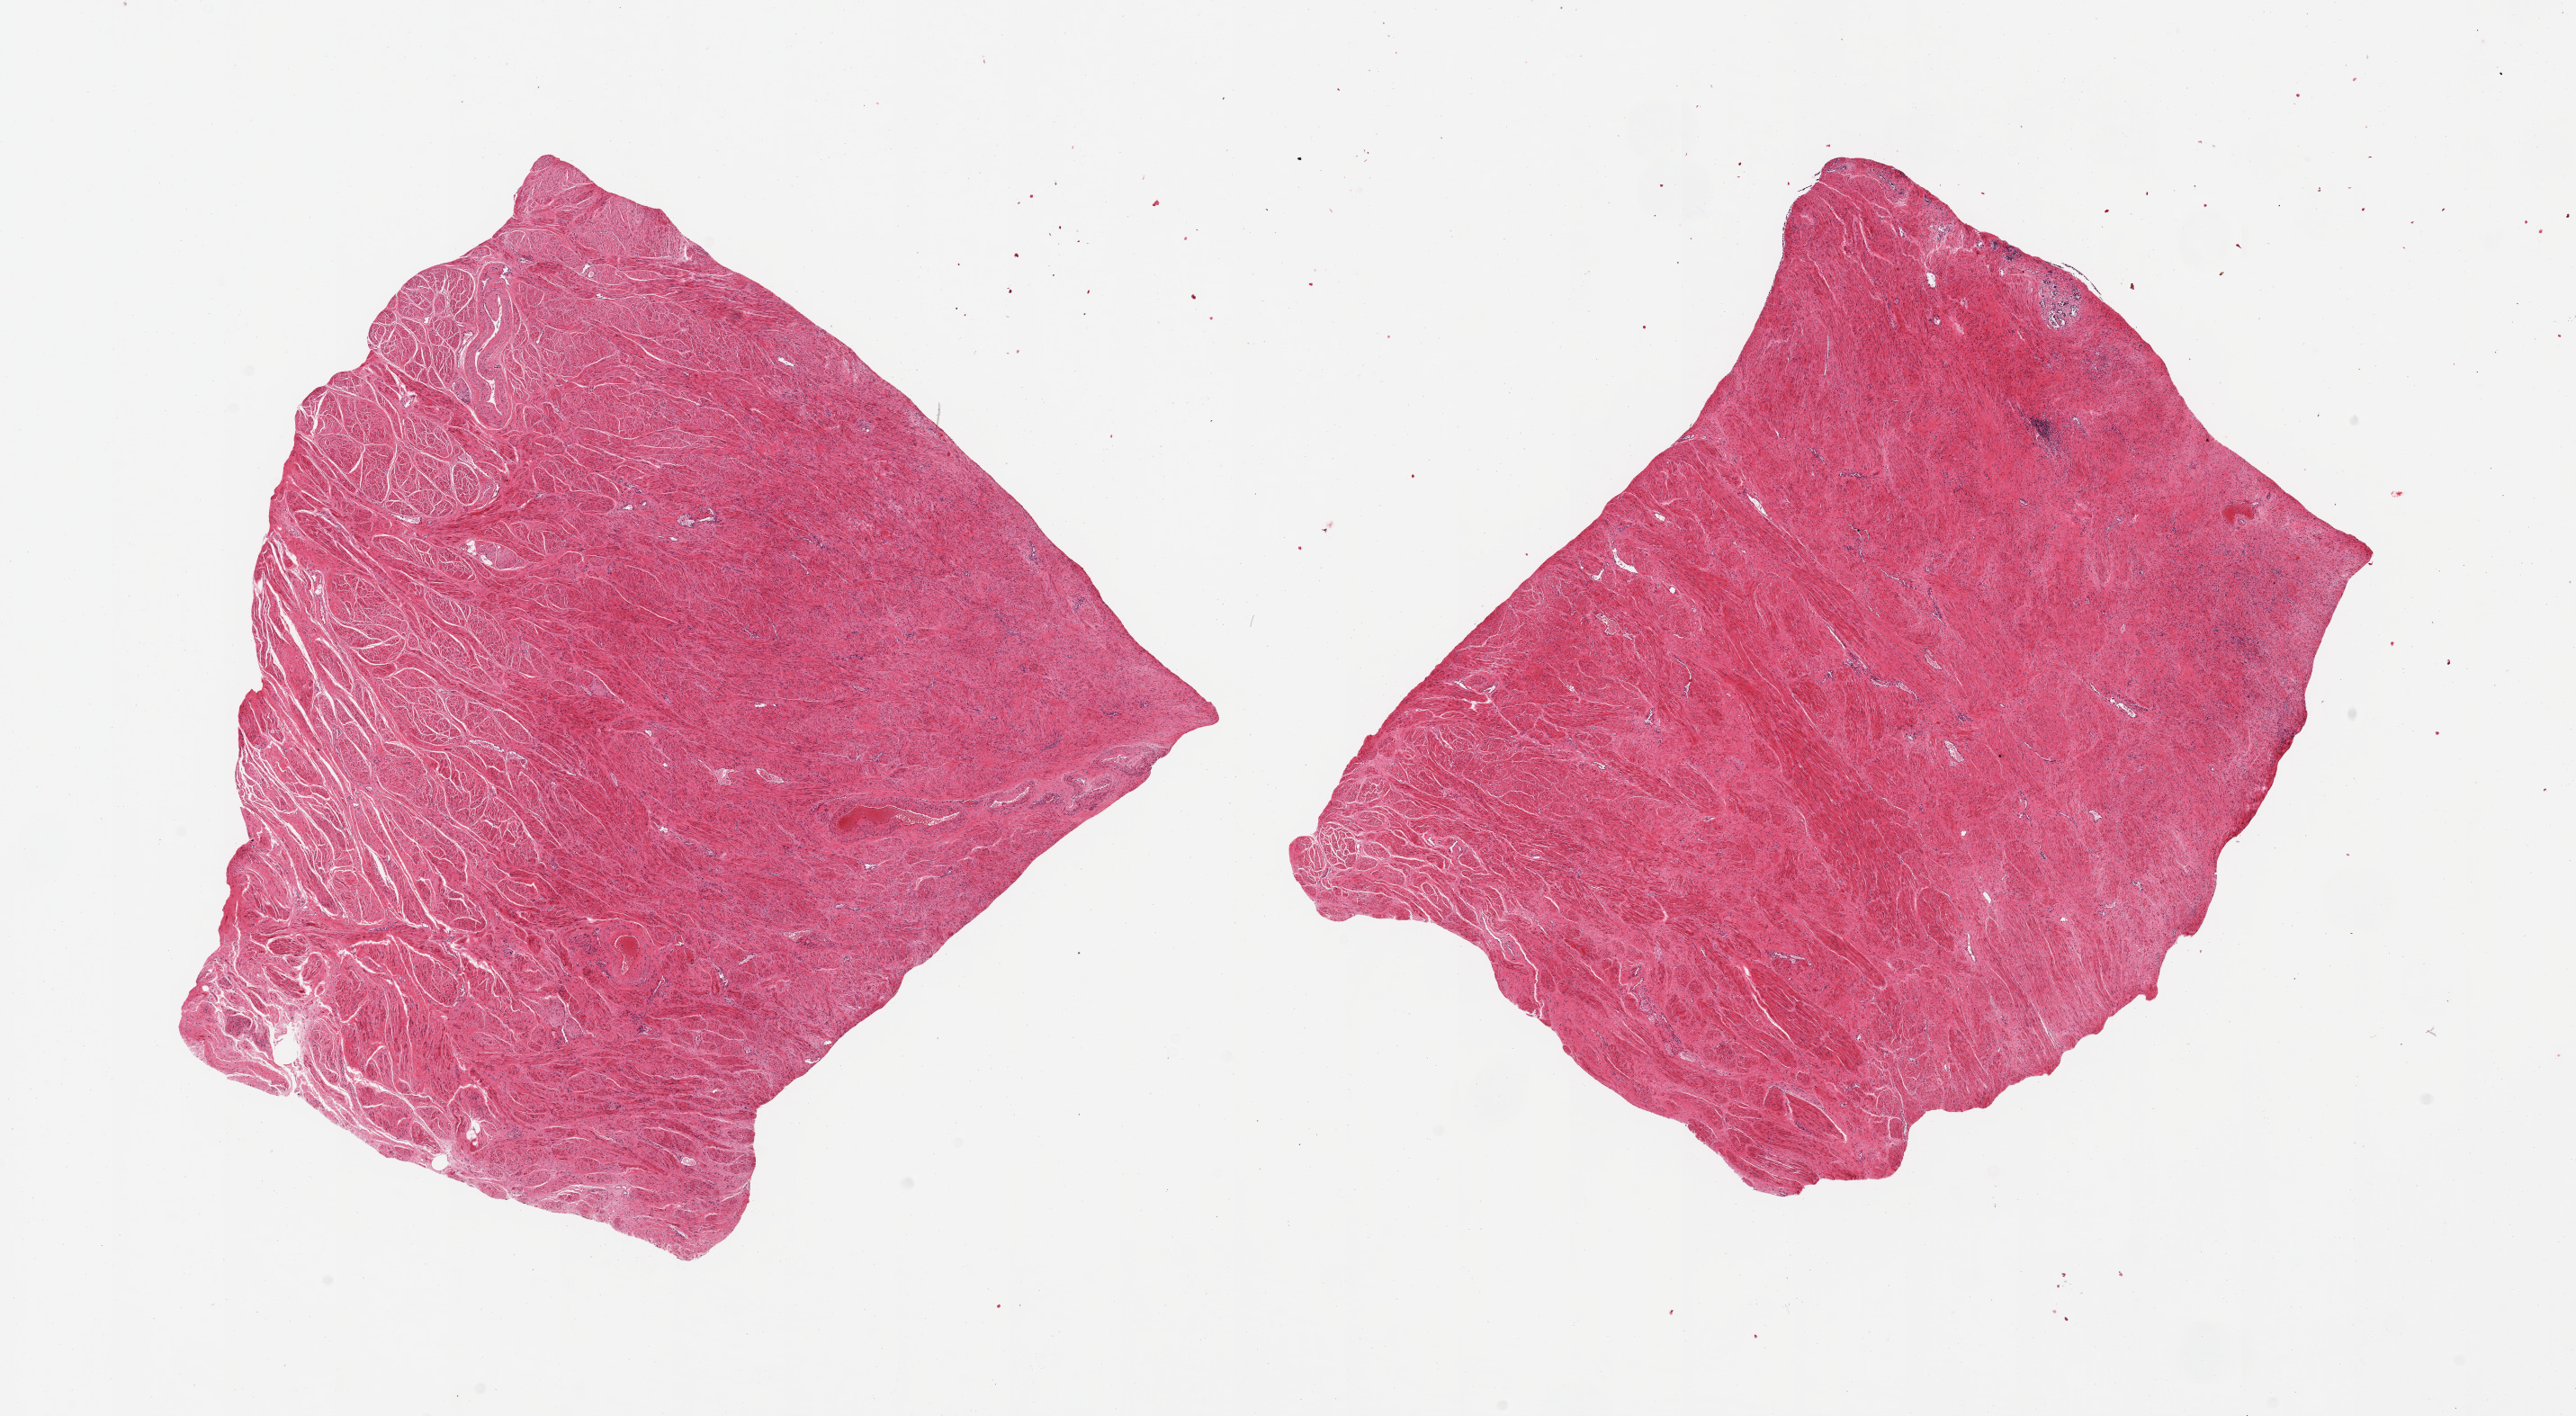
Haematoxylin and eosin whole-slide image — whole scanned area (about 22.6 x 12.4 mm) shown as a low-resolution overview, PAXgene-fixed paraffin-embedded (PFPE) section, sampled site (target tissue): prostate, donor tissue sample. Donor sex: male.
* review note (as recorded): 2 pieces, mainly stroma, few minute glands totally autolyzed